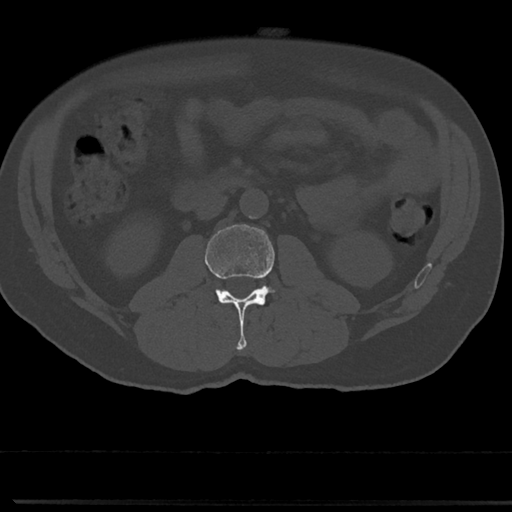
CT including the spine, one axial slice. Position 6 of 817 along the scan axis. Reconstruction kernel Br40s/3. Bone window (W 1800 / L 400 HU). 0.5 mm slice thickness. 512 × 512 image matrix, field of view 355 × 355 mm. Male patient, age 61 years. Case-level facts recorded for this patient, not image findings: primary cancer: prostate.
Annotated regions visible in this slice (semi-automatically segmented with operator editing):
- L2 vertebra: bounding box (x1, y1, x2, y2) in pixels: (205, 225, 280, 350)